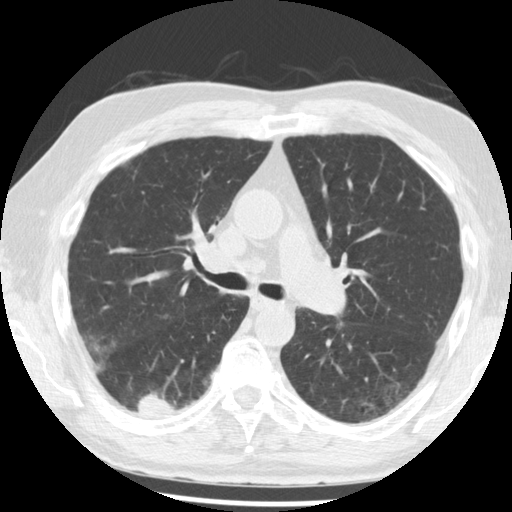
Low-dose screening chest CT, one axial slice; slice 129 of 221 in the series (ordered by position); reconstruction kernel STANDARD; lung window (W 1500 / L -600 HU); 2.5 mm slice thickness; 512 × 512 image matrix.
Annotated regions visible in this slice (outlined manually by an expert reader):
- lesion 1 (tumor, lower lobe of right lung): bounding box (x1, y1, x2, y2) in pixels: (138, 394, 183, 414)